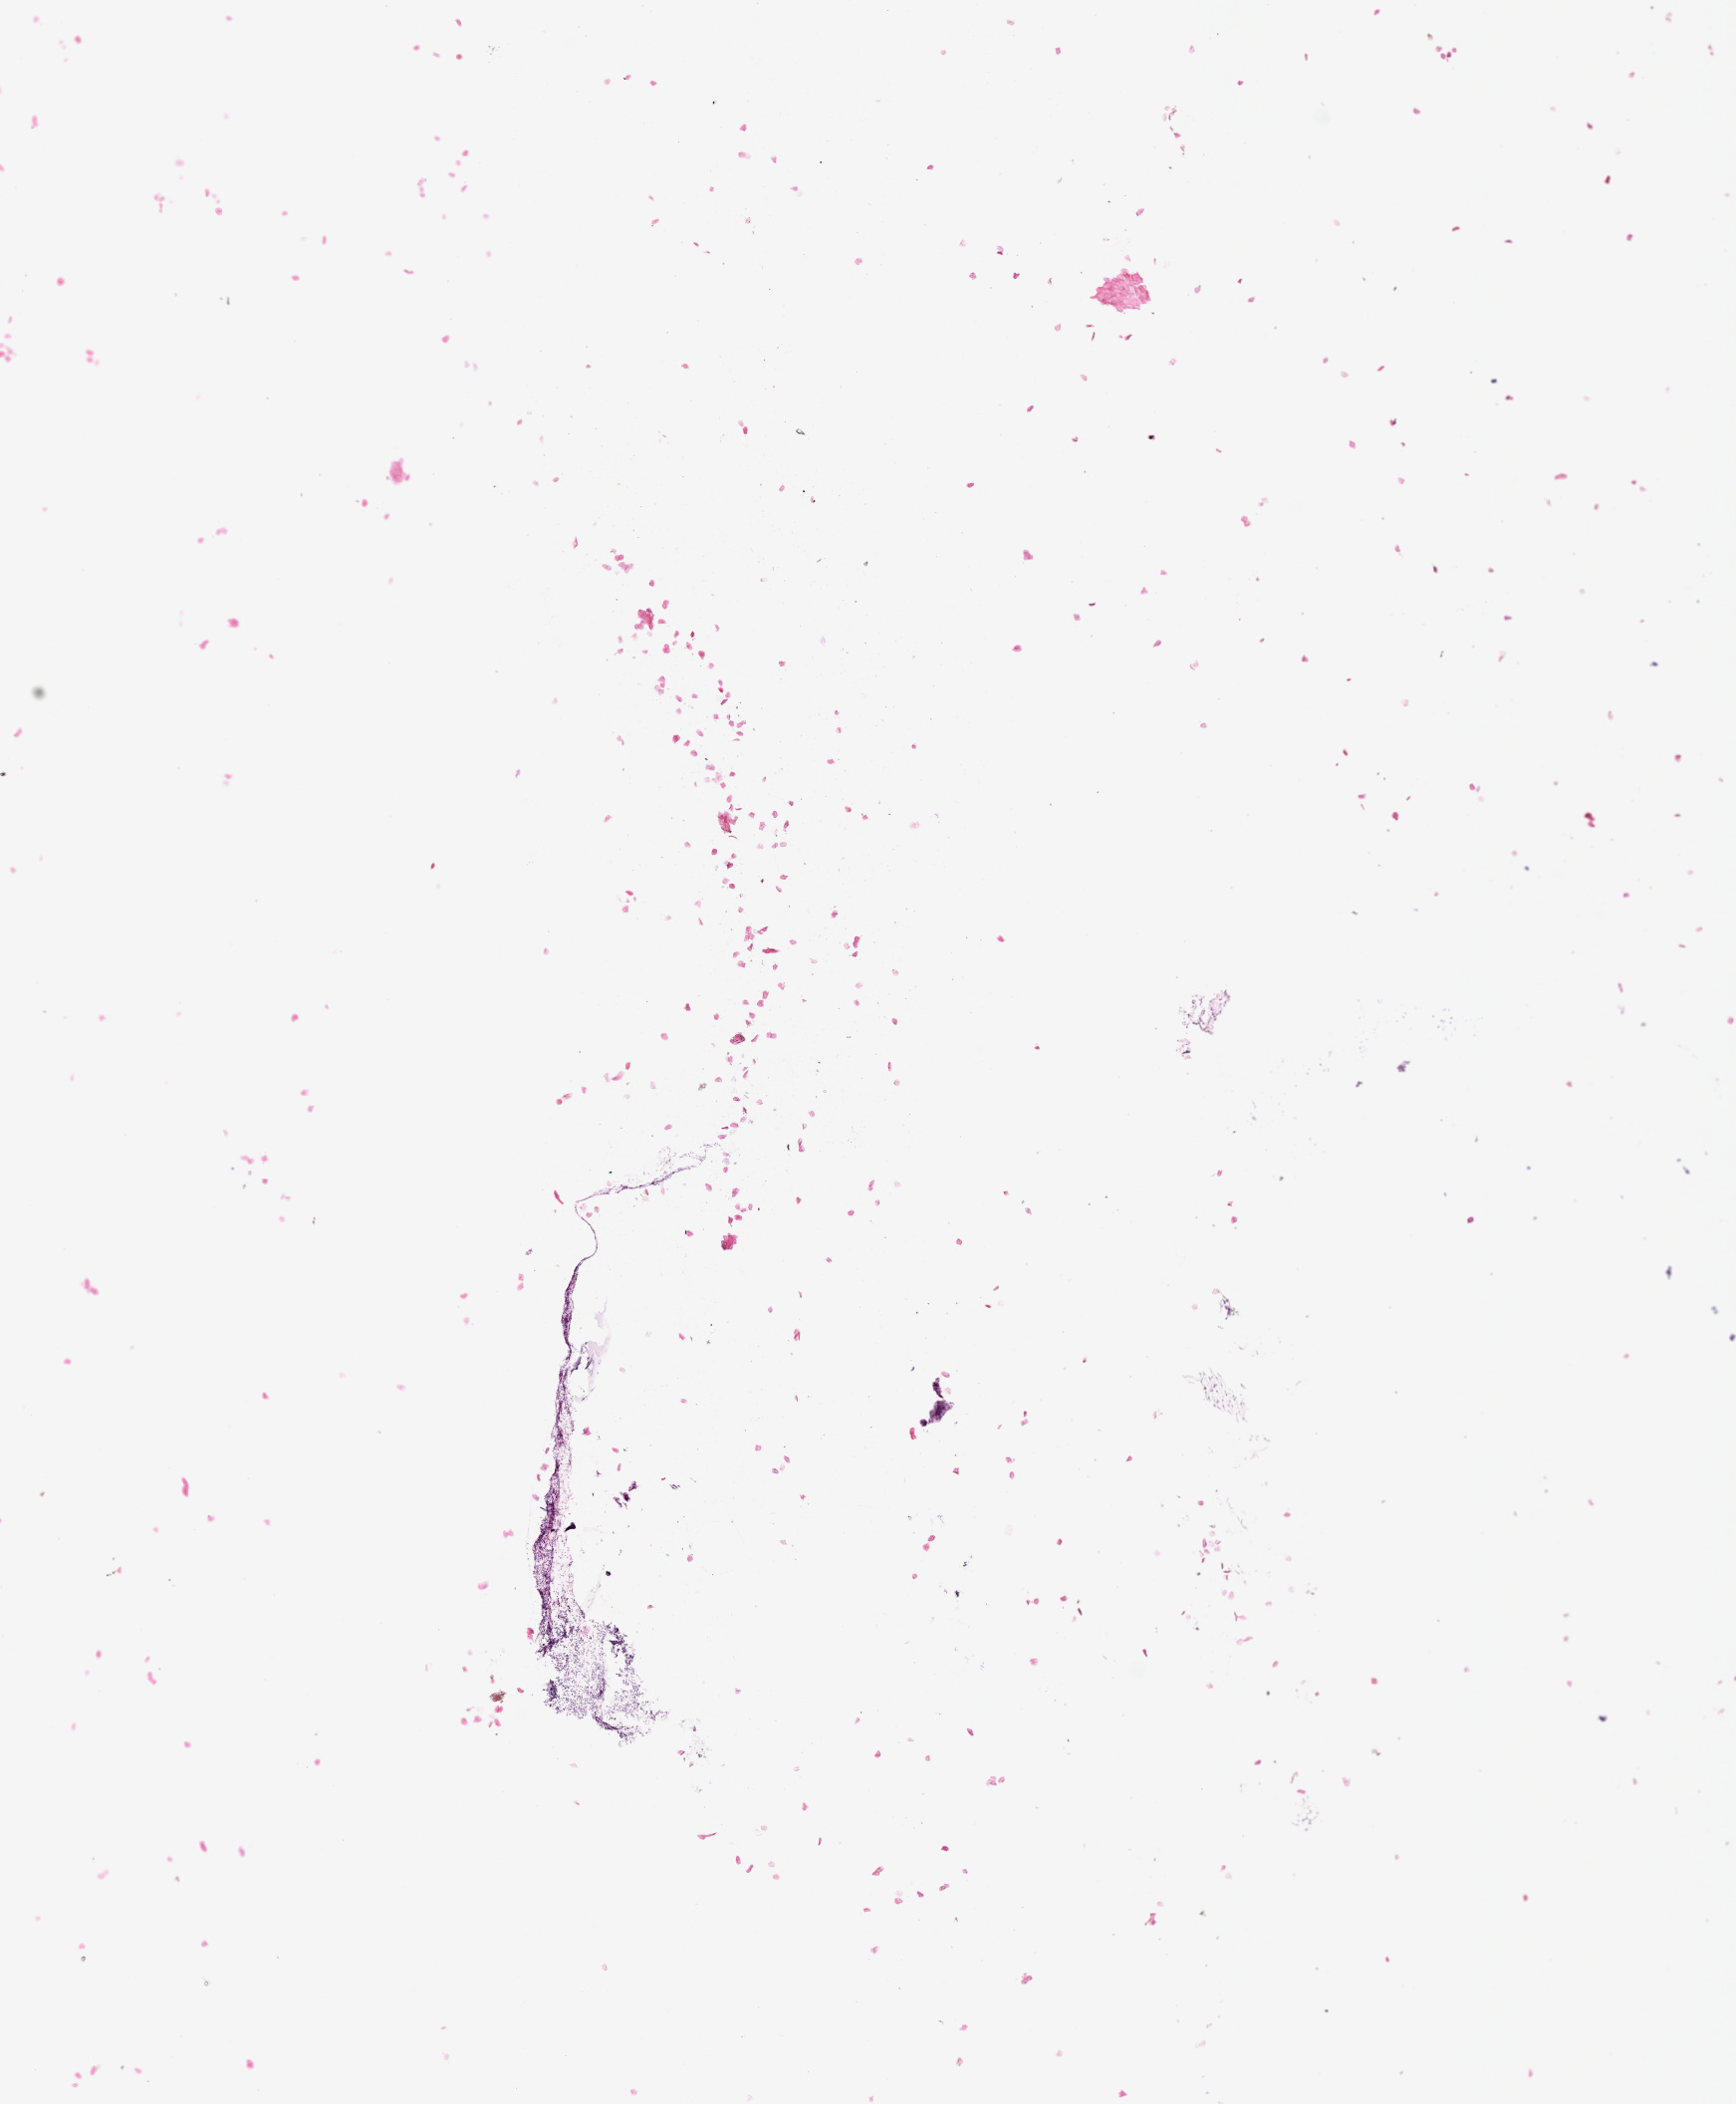
H&E whole-slide image, low-resolution overview of the scanned area, about 7.0 x 8.5 mm (from a 20x scan). Normal (non-tumour) tissue sample, lung. Female, 61 y/o.
This section: normal (non-tumour) tissue from the same patient. Patient diagnosis (cohort enrolment): squamous cell carcinoma (lung).